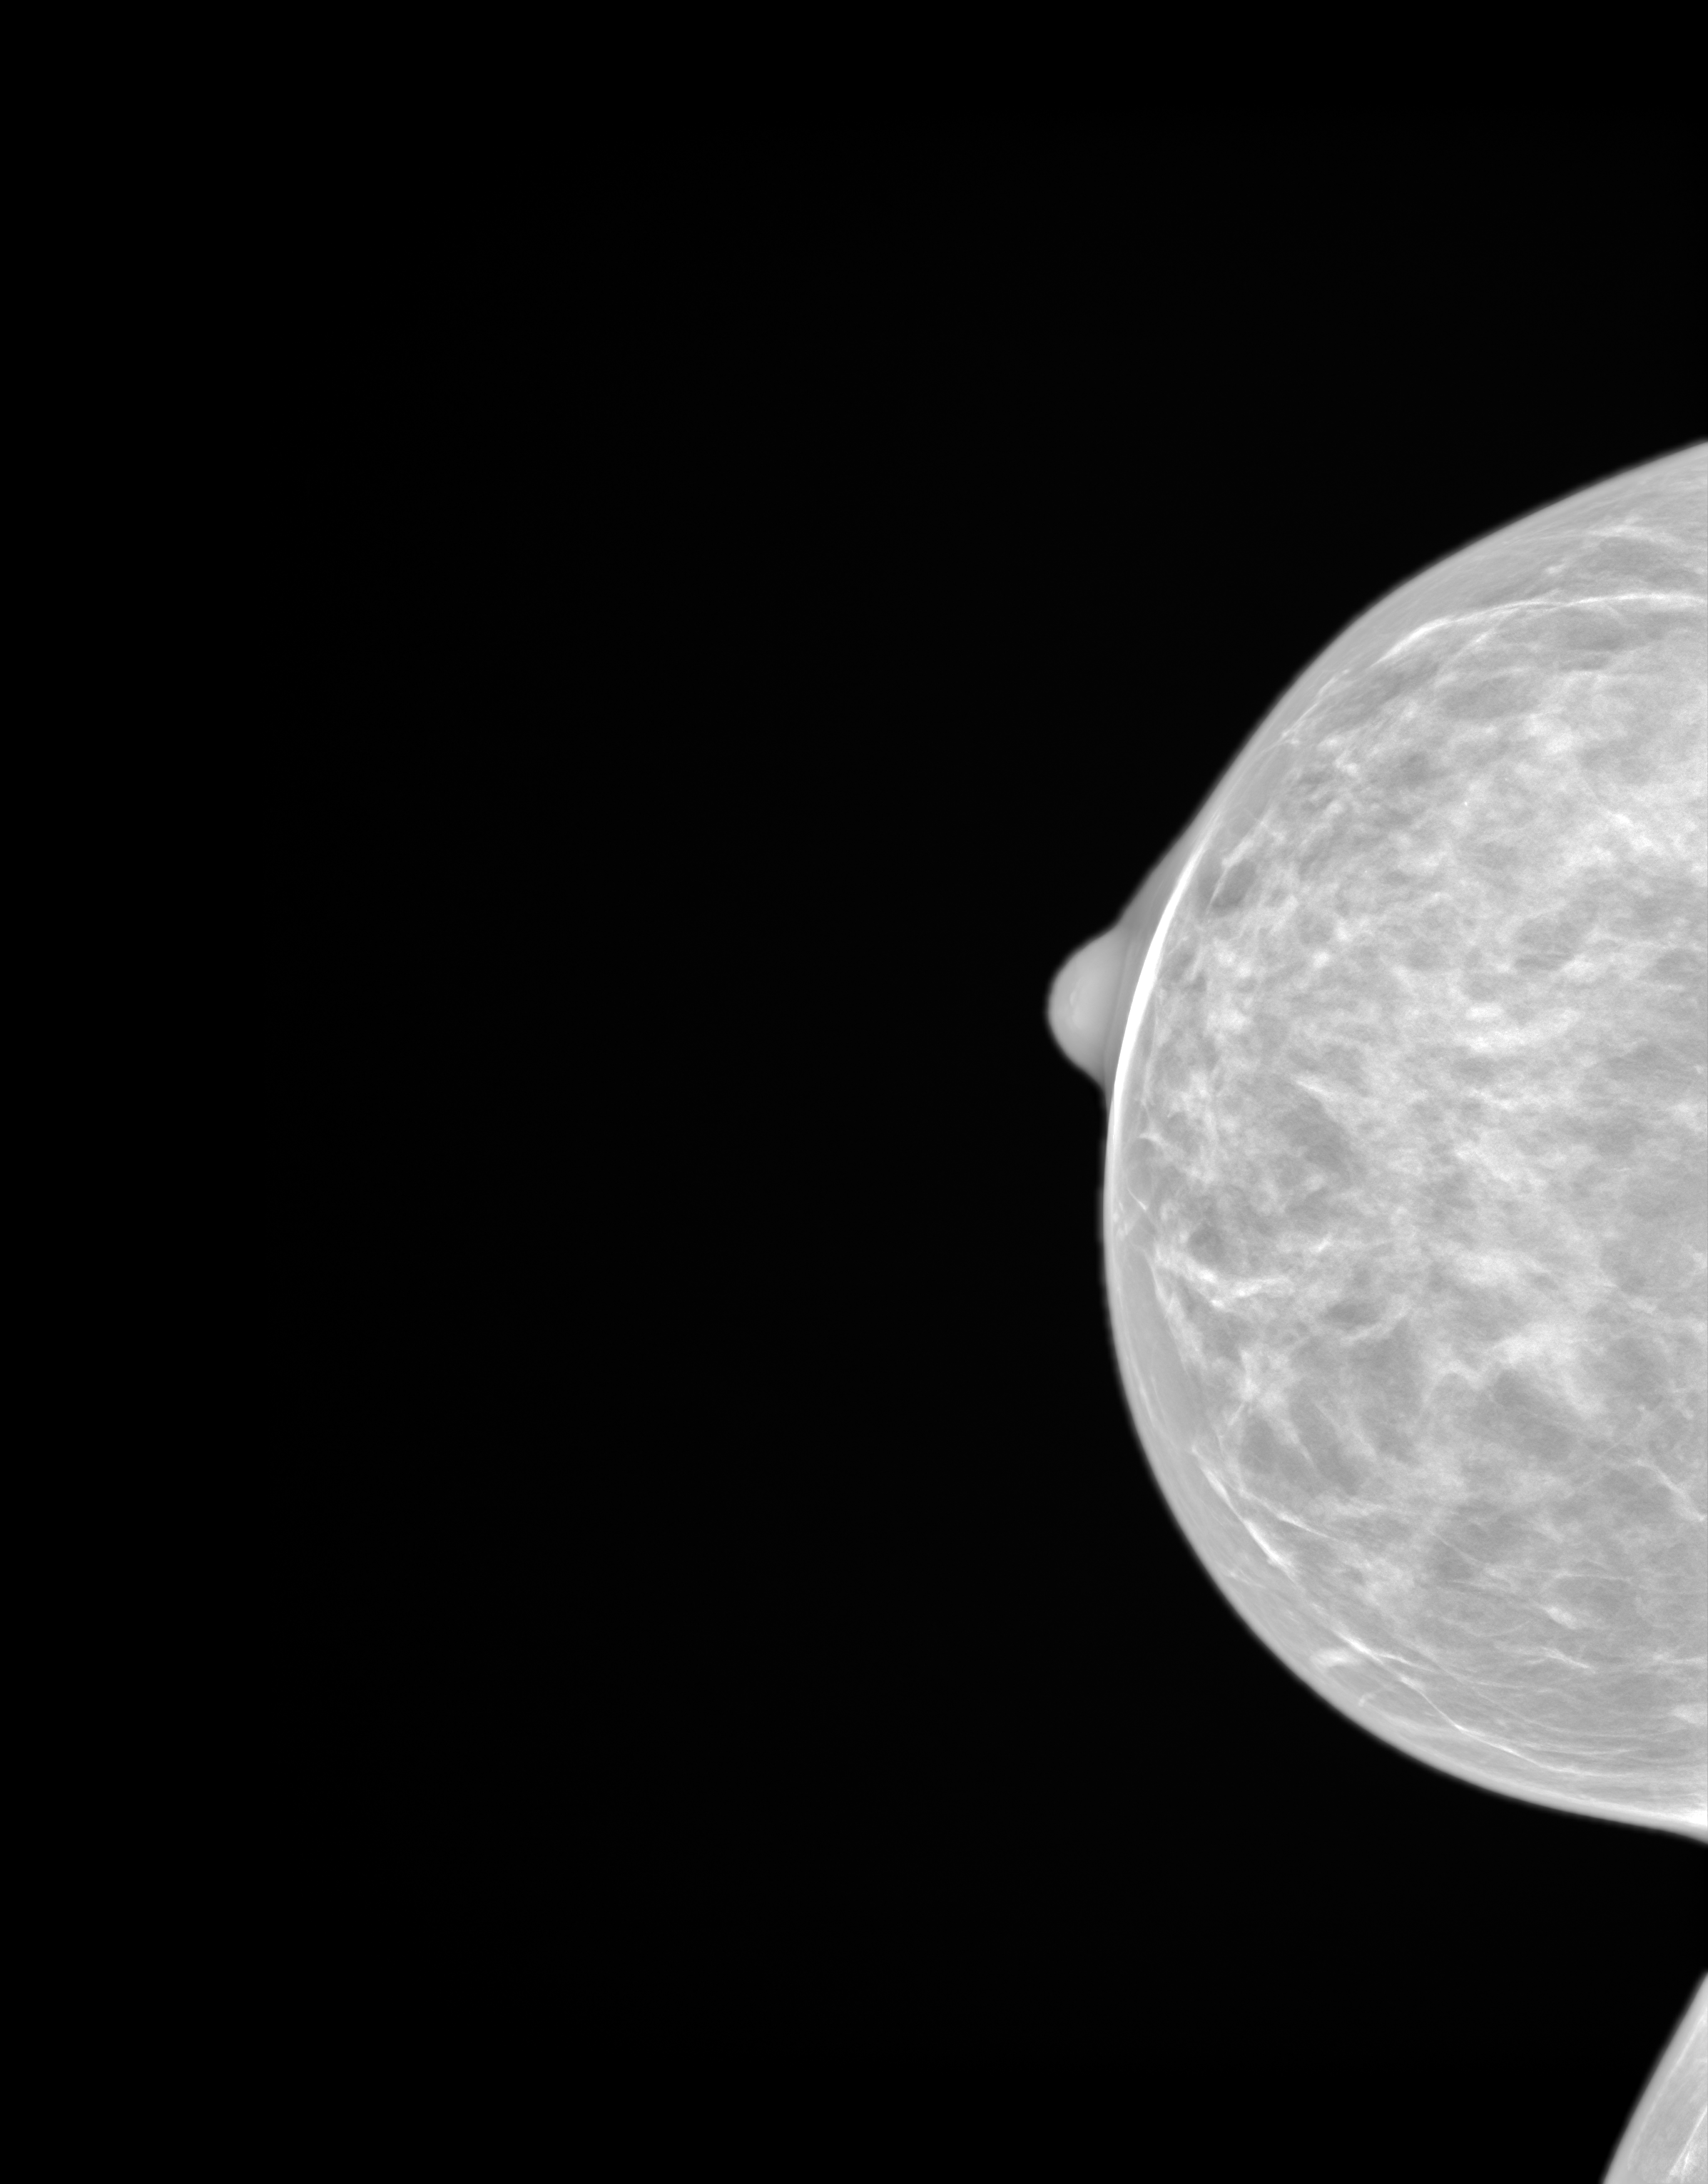
Screening examination. Patient aged 43 years (female).
Image type: synthesized 2-D view from tomosynthesis. Breast: right. Projection: CC view.